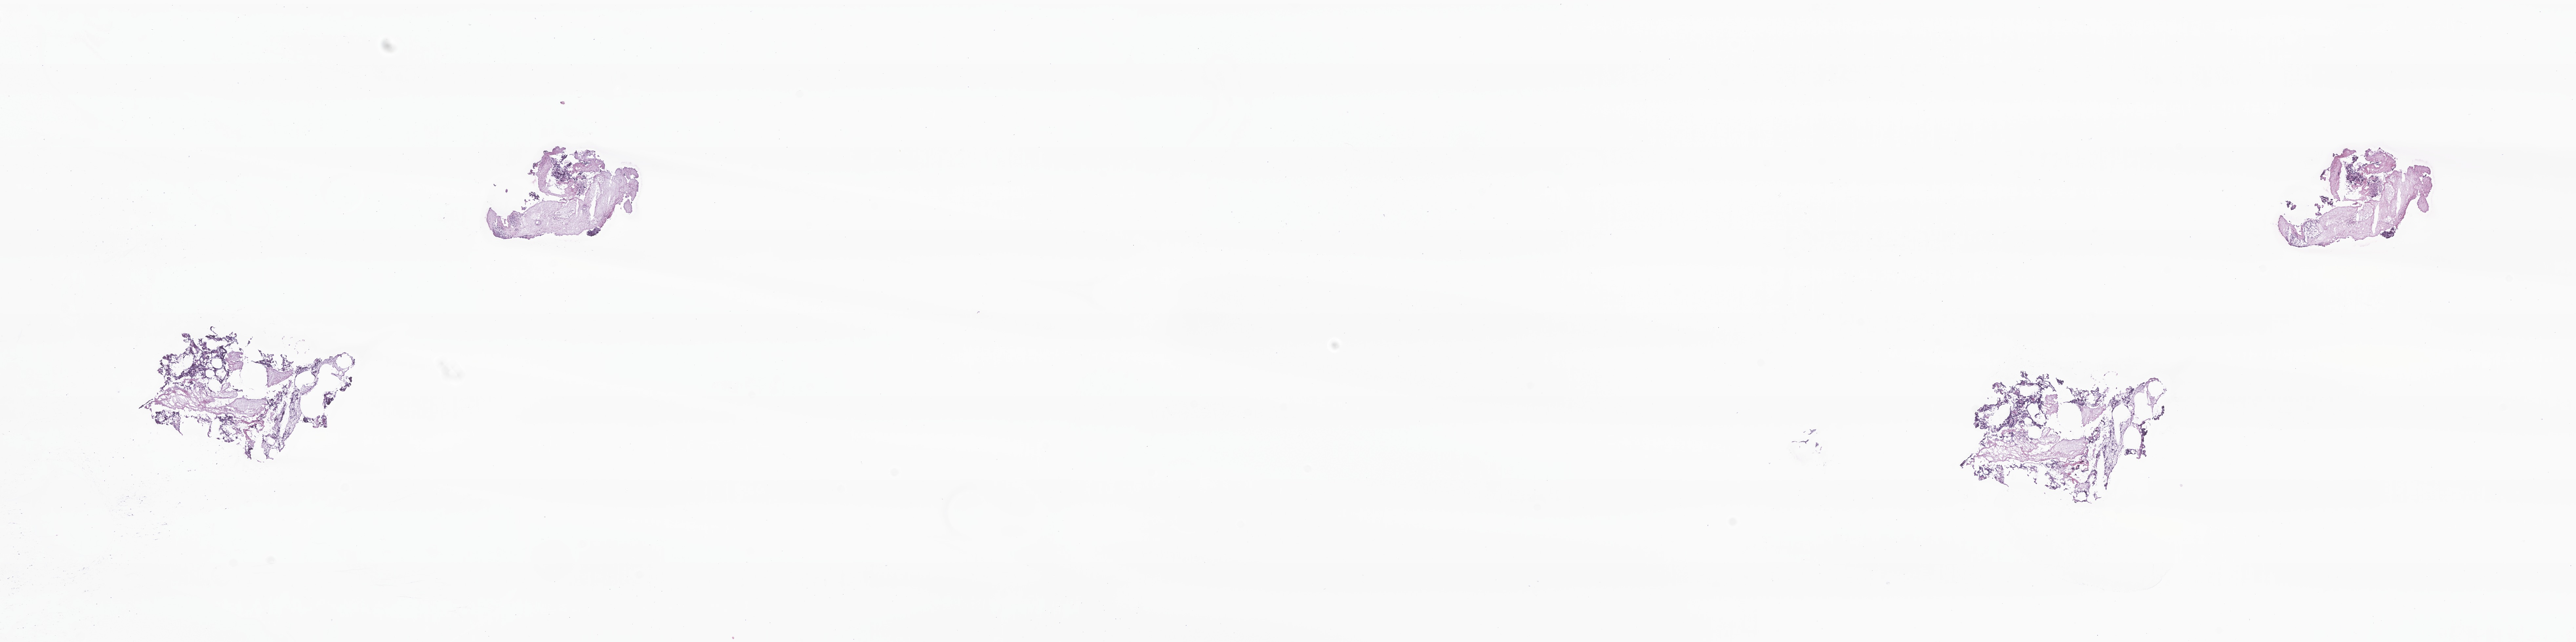
Digitized H&E-stained section of tumor tissue from the brain — shown as a low-resolution overview of the whole scanned area (about 33.1 x 8.2 mm); frozen section. Patient: male, age 121 months (10 years 1 month).
- diagnosis (ICD-O-3 morphology term): Medulloblastoma, NOS